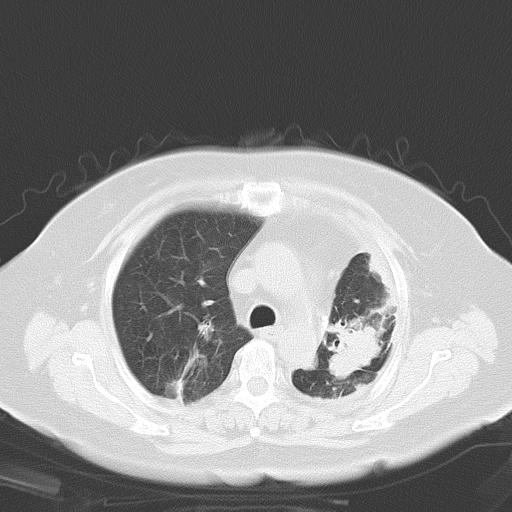
Chest CT, one axial slice; slice 21 of 29 in the series (ordered by position); lung window (W 1500 / L -600 HU); 8 mm slice thickness; 512 × 512 image matrix, field of view 347 × 347 mm. Patient: female, 69 years. From the clinical record (not read from this slice): clinical TNM (as recorded): T3 N0 M0.
Annotated regions visible in this slice (rectangle marked by the reading radiologist):
- lung tumour (recorded histology: adenocarcinoma): box from (x=334, y=318) to (x=381, y=380) px